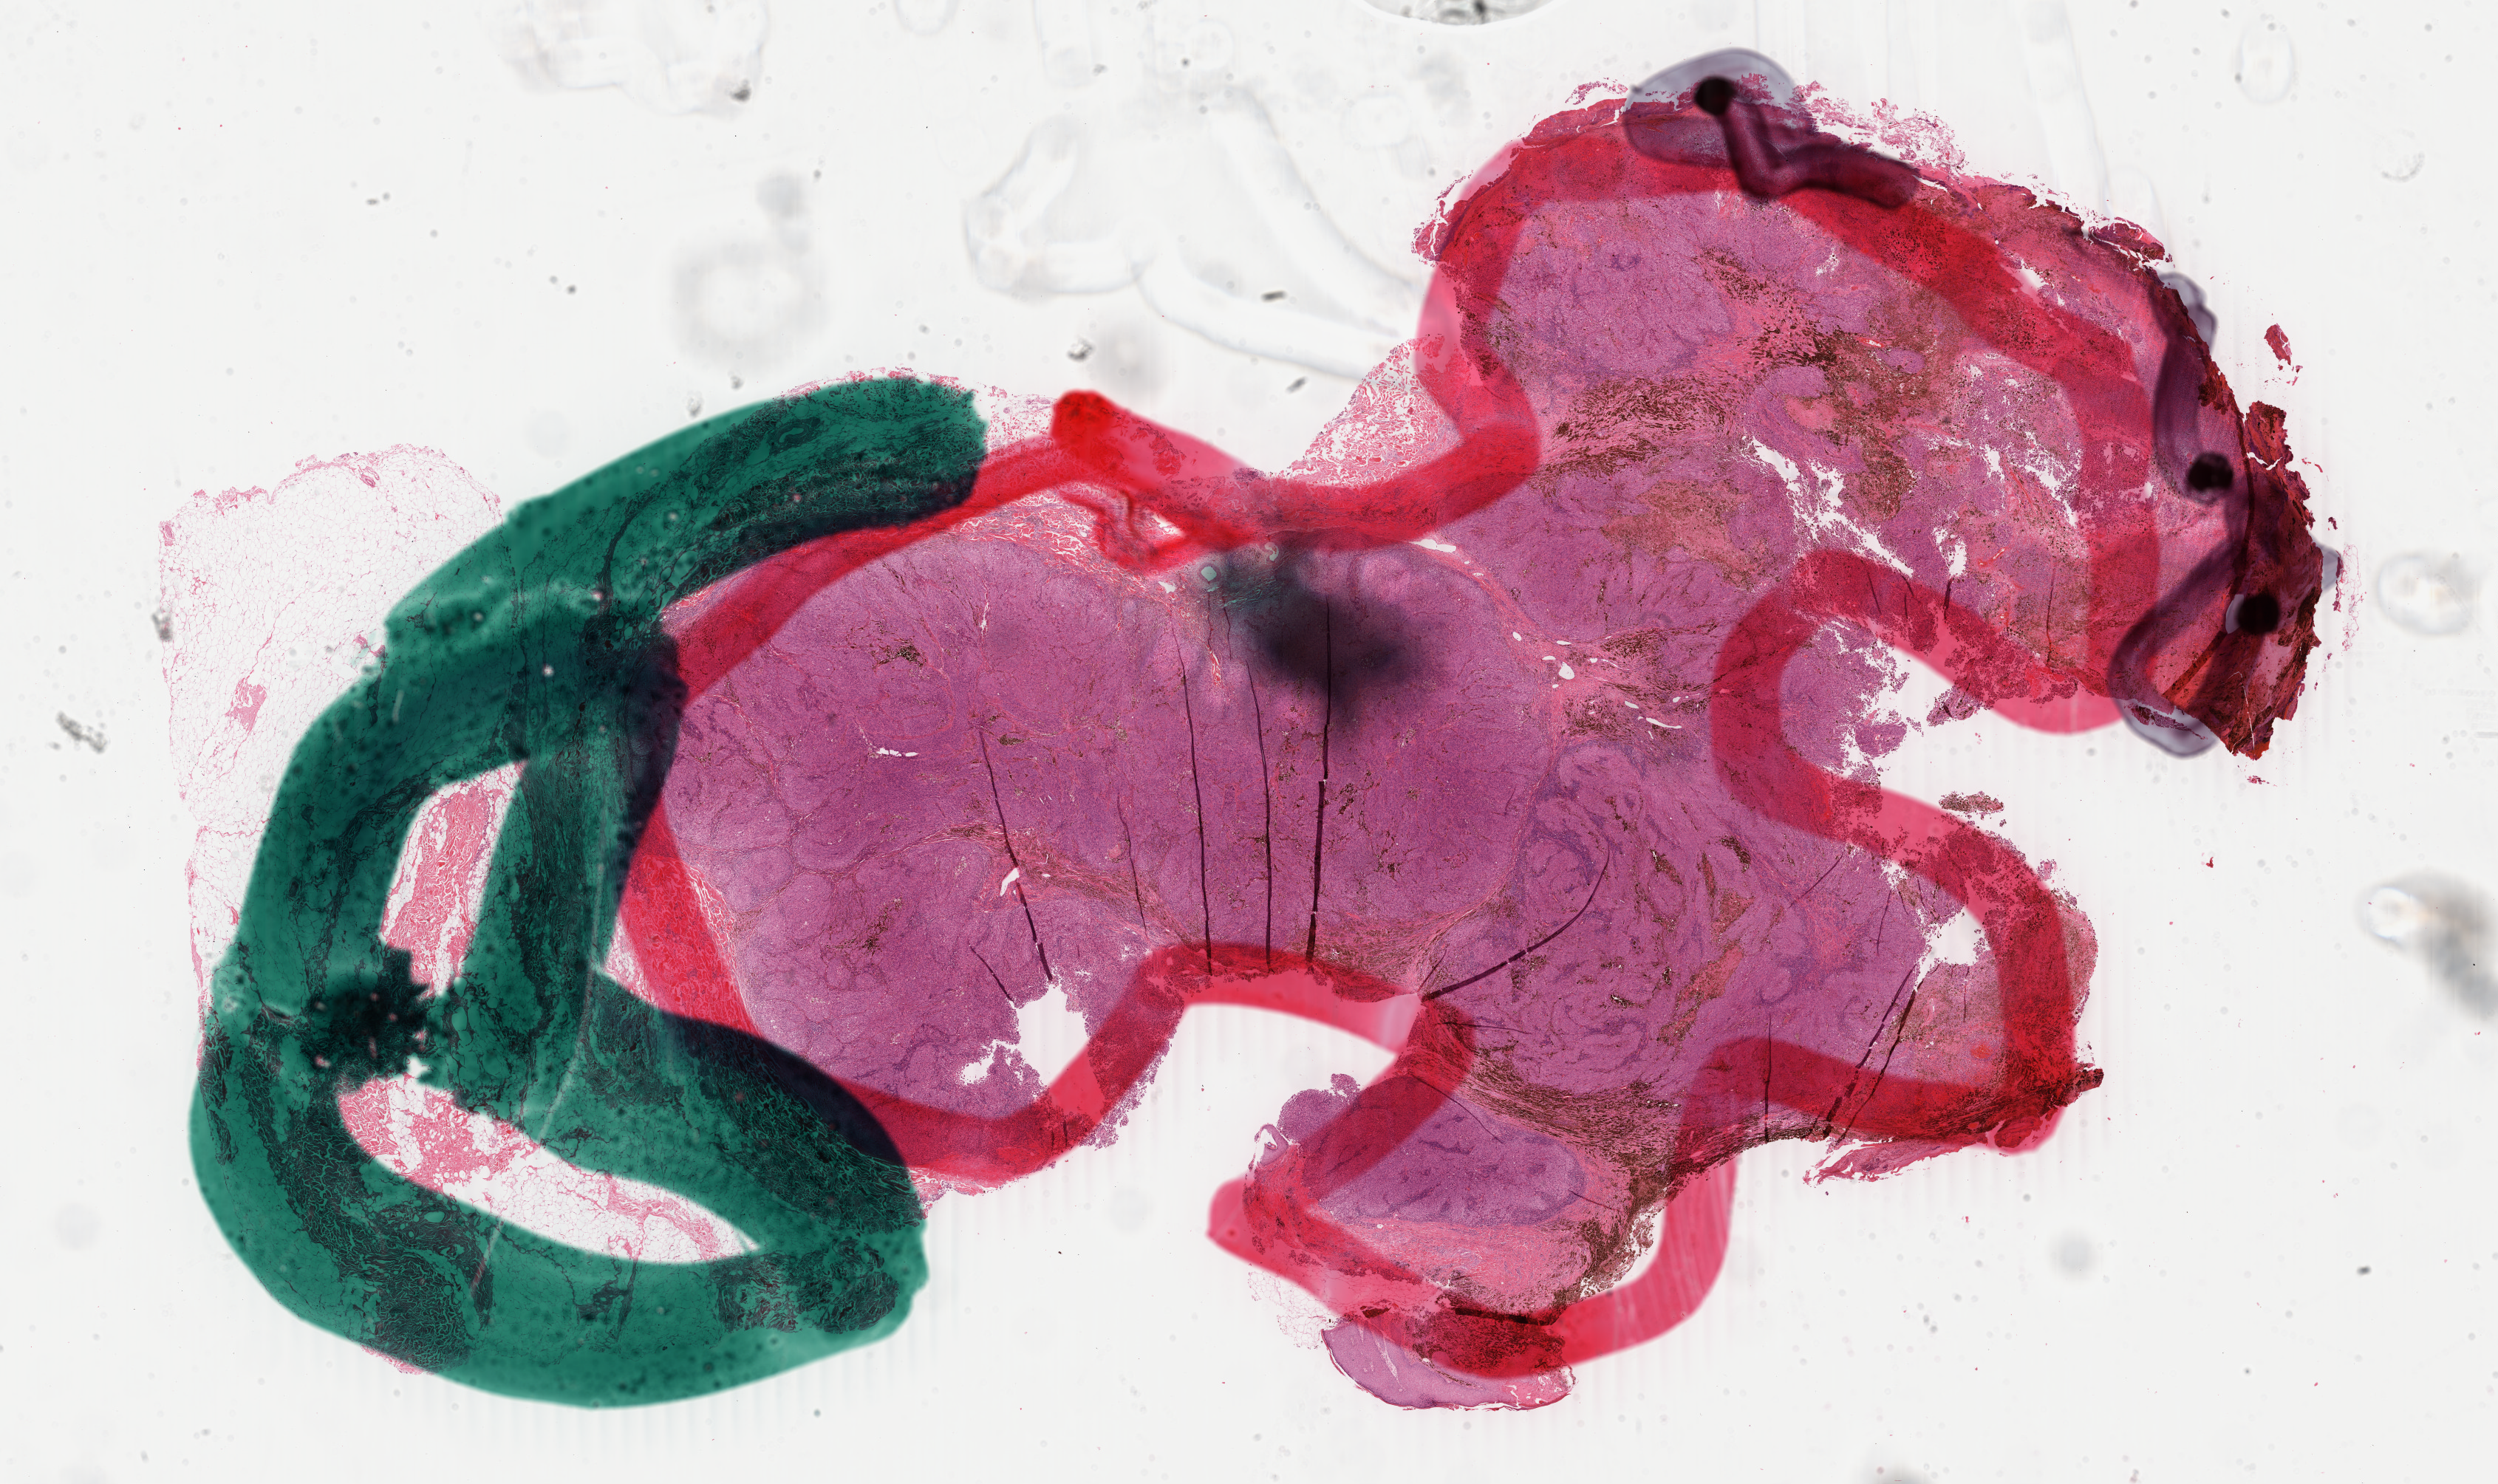
Whole-slide histology image, H&E — whole scanned area (about 26.9 x 16.0 mm, slide scanned at 40x) shown as a low-resolution overview. Formalin-fixed paraffin-embedded (FFPE) diagnostic section. Primary tumour sample from the skin. Patient: male, age at initial diagnosis 66 years.
Histologic diagnosis: Malignant melanoma, NOS.